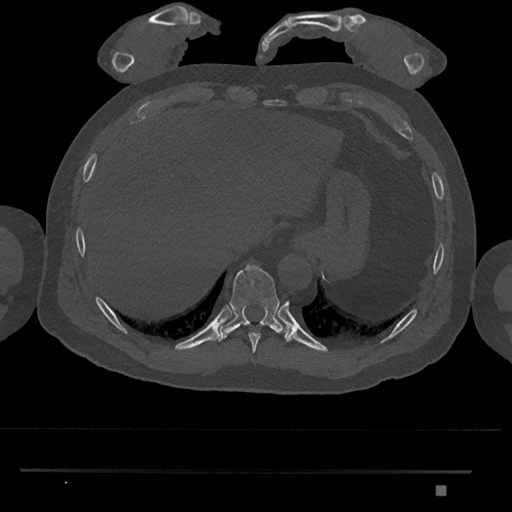
CT including the spine, one axial slice; position 1019 of 1134 along the scan axis; reconstruction kernel Br40s/3; 120 kVp; bone window (W 1800 / L 400 HU); 512 × 512 image matrix, field of view 429 × 429 mm. Male patient, age 65 years. From the clinical record (not read from this slice): primary cancer: prostate.
Structures marked on this image (semi-automatically segmented with operator editing):
- T10 vertebra: bounding box <217,264,287,343> (left, top, right, bottom; pixels)
- T9 vertebra: <248,333,261,353>